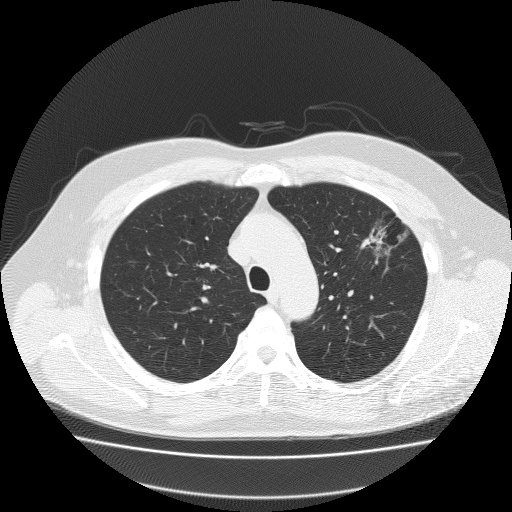
Low-dose screening chest CT, one axial slice; position 151 of 204 along the scan axis; reconstruction kernel FC51; lung window (W 1500 / L -600 HU); 2 mm slice thickness; 512 × 512 image matrix, field of view 410 × 410 mm.
Structures marked on this image (expert manual segmentation):
- lesion 1 (tumor, upper lobe of left lung): box from (x=360, y=224) to (x=388, y=254) px